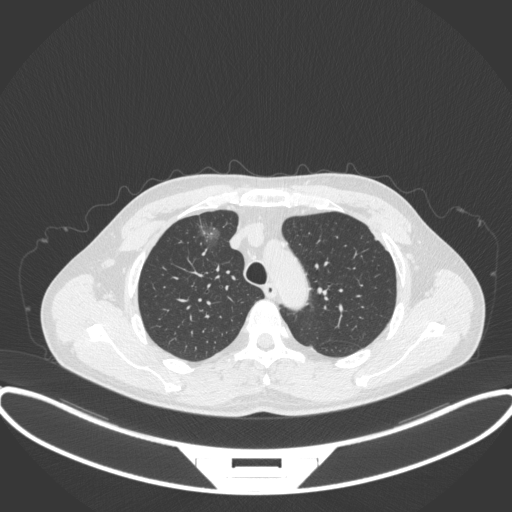
Chest CT, one axial slice. Position 279 of 395 along the scan axis. Reconstruction kernel B31f. Lung window (W 1500 / L -600 HU). 512 × 512 image matrix, field of view 424 × 424 mm. Male patient, age 60 years. From the clinical record (not read from this slice): clinical TNM (as recorded): T1c N0 M0.
Structures marked on this image (rectangle marked by the reading radiologist):
- lung tumour (recorded histology: adenocarcinoma): bounding box (x1, y1, x2, y2) in pixels: (192, 214, 226, 253)